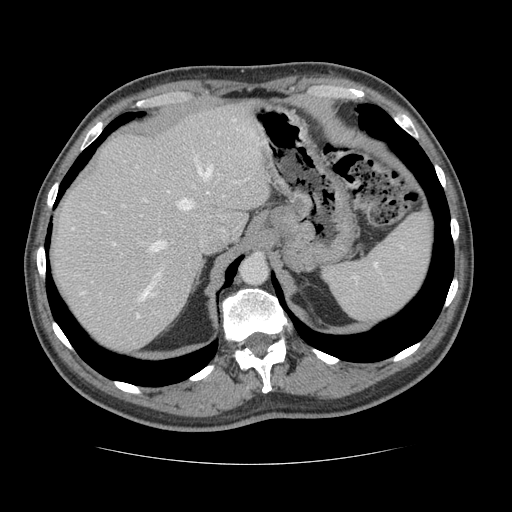
Contrast-enhanced abdominal CT, one axial slice. Slice 99 of 134 in the series (ordered by position). Reconstruction kernel STANDARD. Intravenous contrast given. Soft-tissue window (W 400 / L 40 HU). 512 × 512 image matrix. Male patient, age 68 years. Case-level facts recorded for this patient, not image findings: diagnosis: colorectal cancer liver metastases, imaged before liver resection; multiple liver metastases: yes; largest metastasis: 2.2 cm; disease in both lobes: no.
Structures marked on this image (expert manual segmentation):
- hepatic veins: bounding box (x1, y1, x2, y2) in pixels: (81, 166, 212, 317)
- liver: (52, 103, 269, 352)
- planned liver remnant (the part of the liver to remain after resection): (51, 103, 269, 326)
- portal vein (with intrahepatic branches): (113, 243, 154, 296)